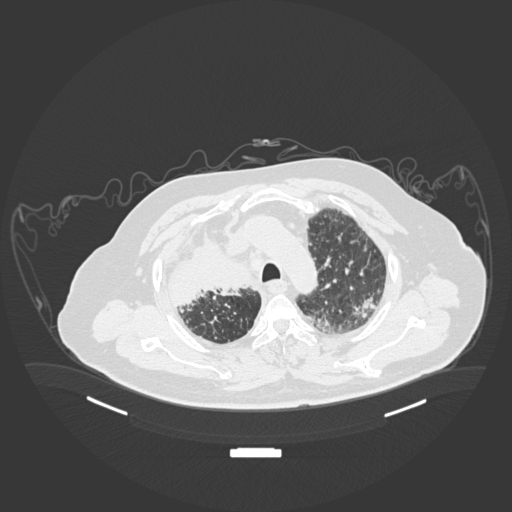
Chest CT, one axial slice. Slice 145 of 201 in the series (ordered by position). Lung window (W 1500 / L -600 HU). 1 mm slice thickness. 512 × 512 image matrix, field of view 500 × 500 mm. Patient: male, 69 years. From the clinical record (not read from this slice): clinical TNM (as recorded): T4 N3 M1.
Annotated regions visible in this slice (rectangle marked by the reading radiologist):
- lung tumour (recorded histology: adenocarcinoma): bounding box [x1, y1, x2, y2] px = [165, 221, 259, 309]